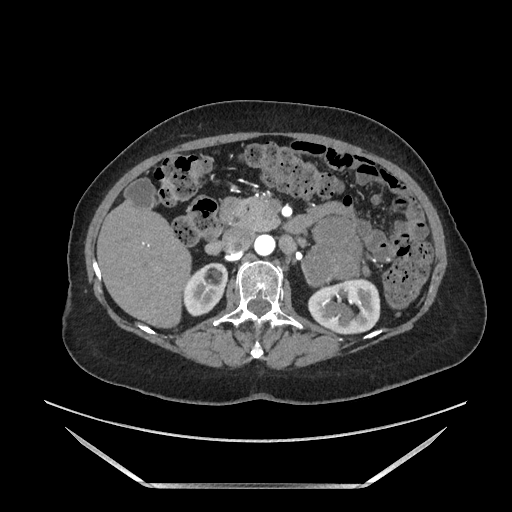
Contrast-enhanced abdominal CT, one axial slice; slice 89 of 205 in the series (ordered by position); soft-tissue window (W 400 / L 40 HU); 512 × 512 image matrix, field of view 440 × 440 mm. Female patient. From the clinical record (not read from this slice): diagnosis: adrenocortical carcinoma; tumour side: left adrenal; tumour size at pathology: 12.5 cm; Ki-67 index: 39 %; stage (as recorded): 3.
Annotated regions visible in this slice (semi-automatically segmented with operator editing):
- mass: bounding box (x1, y1, x2, y2) in pixels: (303, 220, 361, 285)